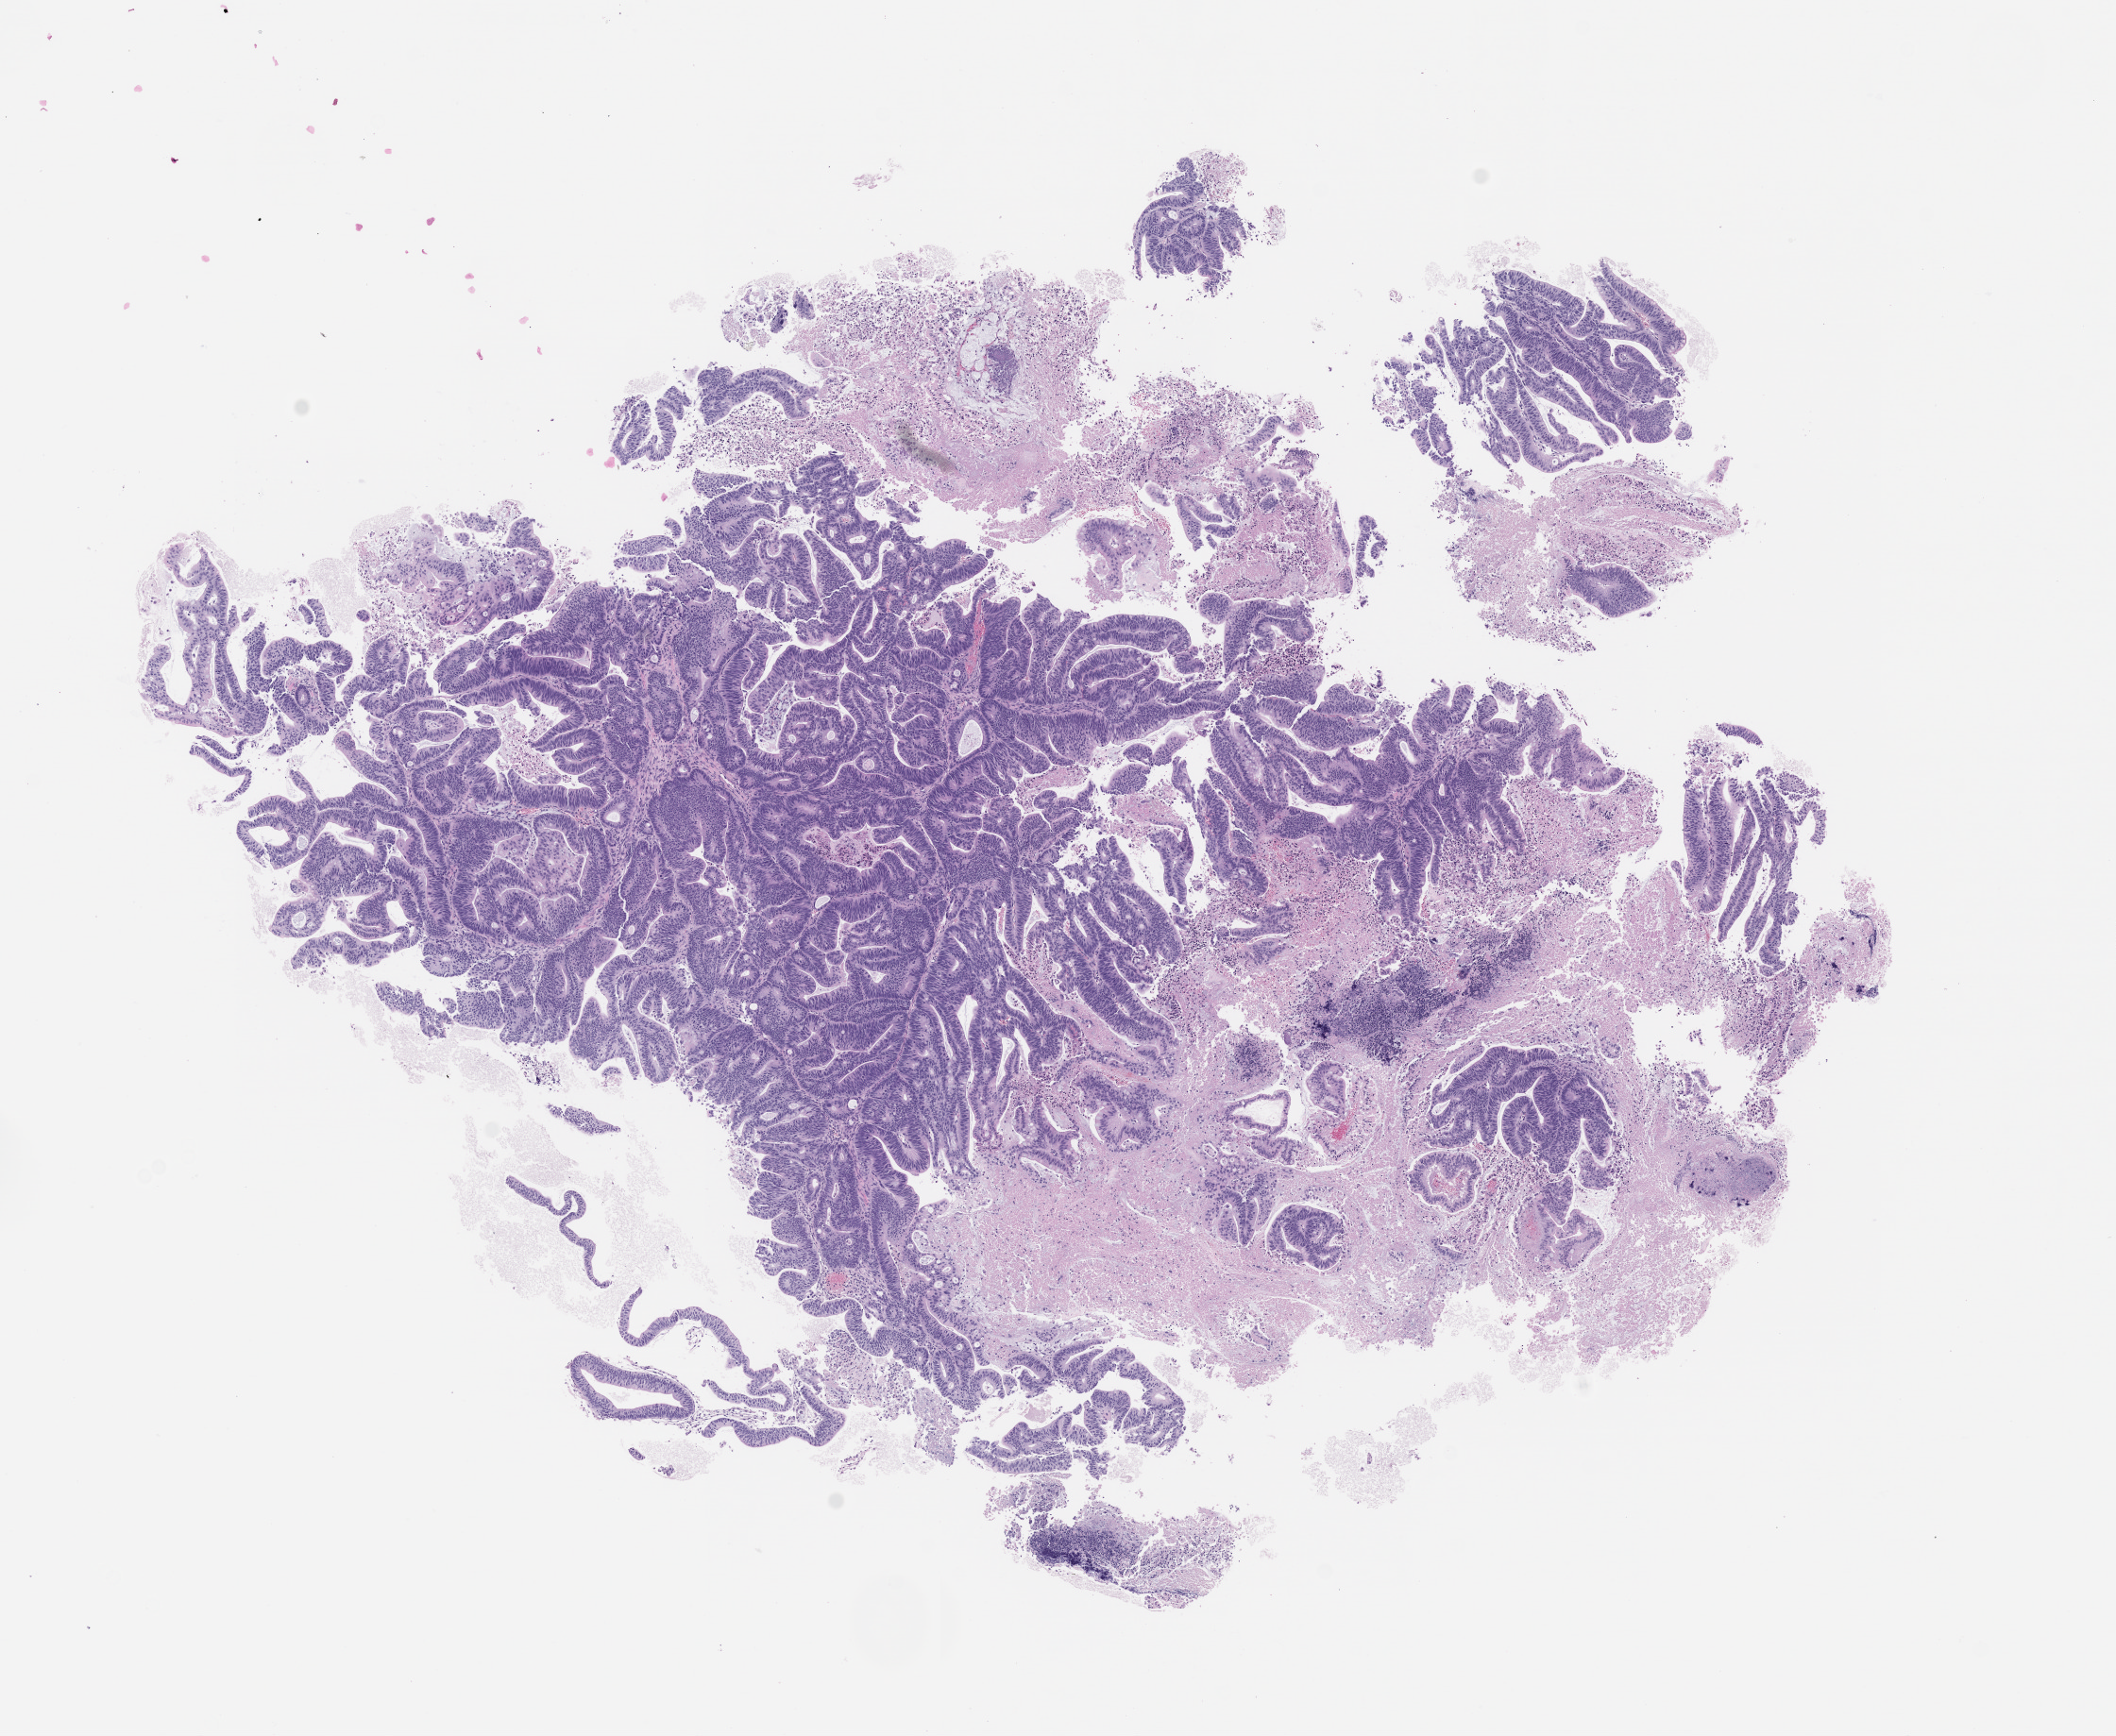
H&E whole-slide image of a patient-derived xenograft (PDX) tumor grown in a mouse, passage 0 — whole scanned area (about 9.0 x 7.4 mm) shown as a low-resolution overview, FFPE section, tumor site category: colon.
Originating patient diagnosis: Colon Adenocarcinoma.